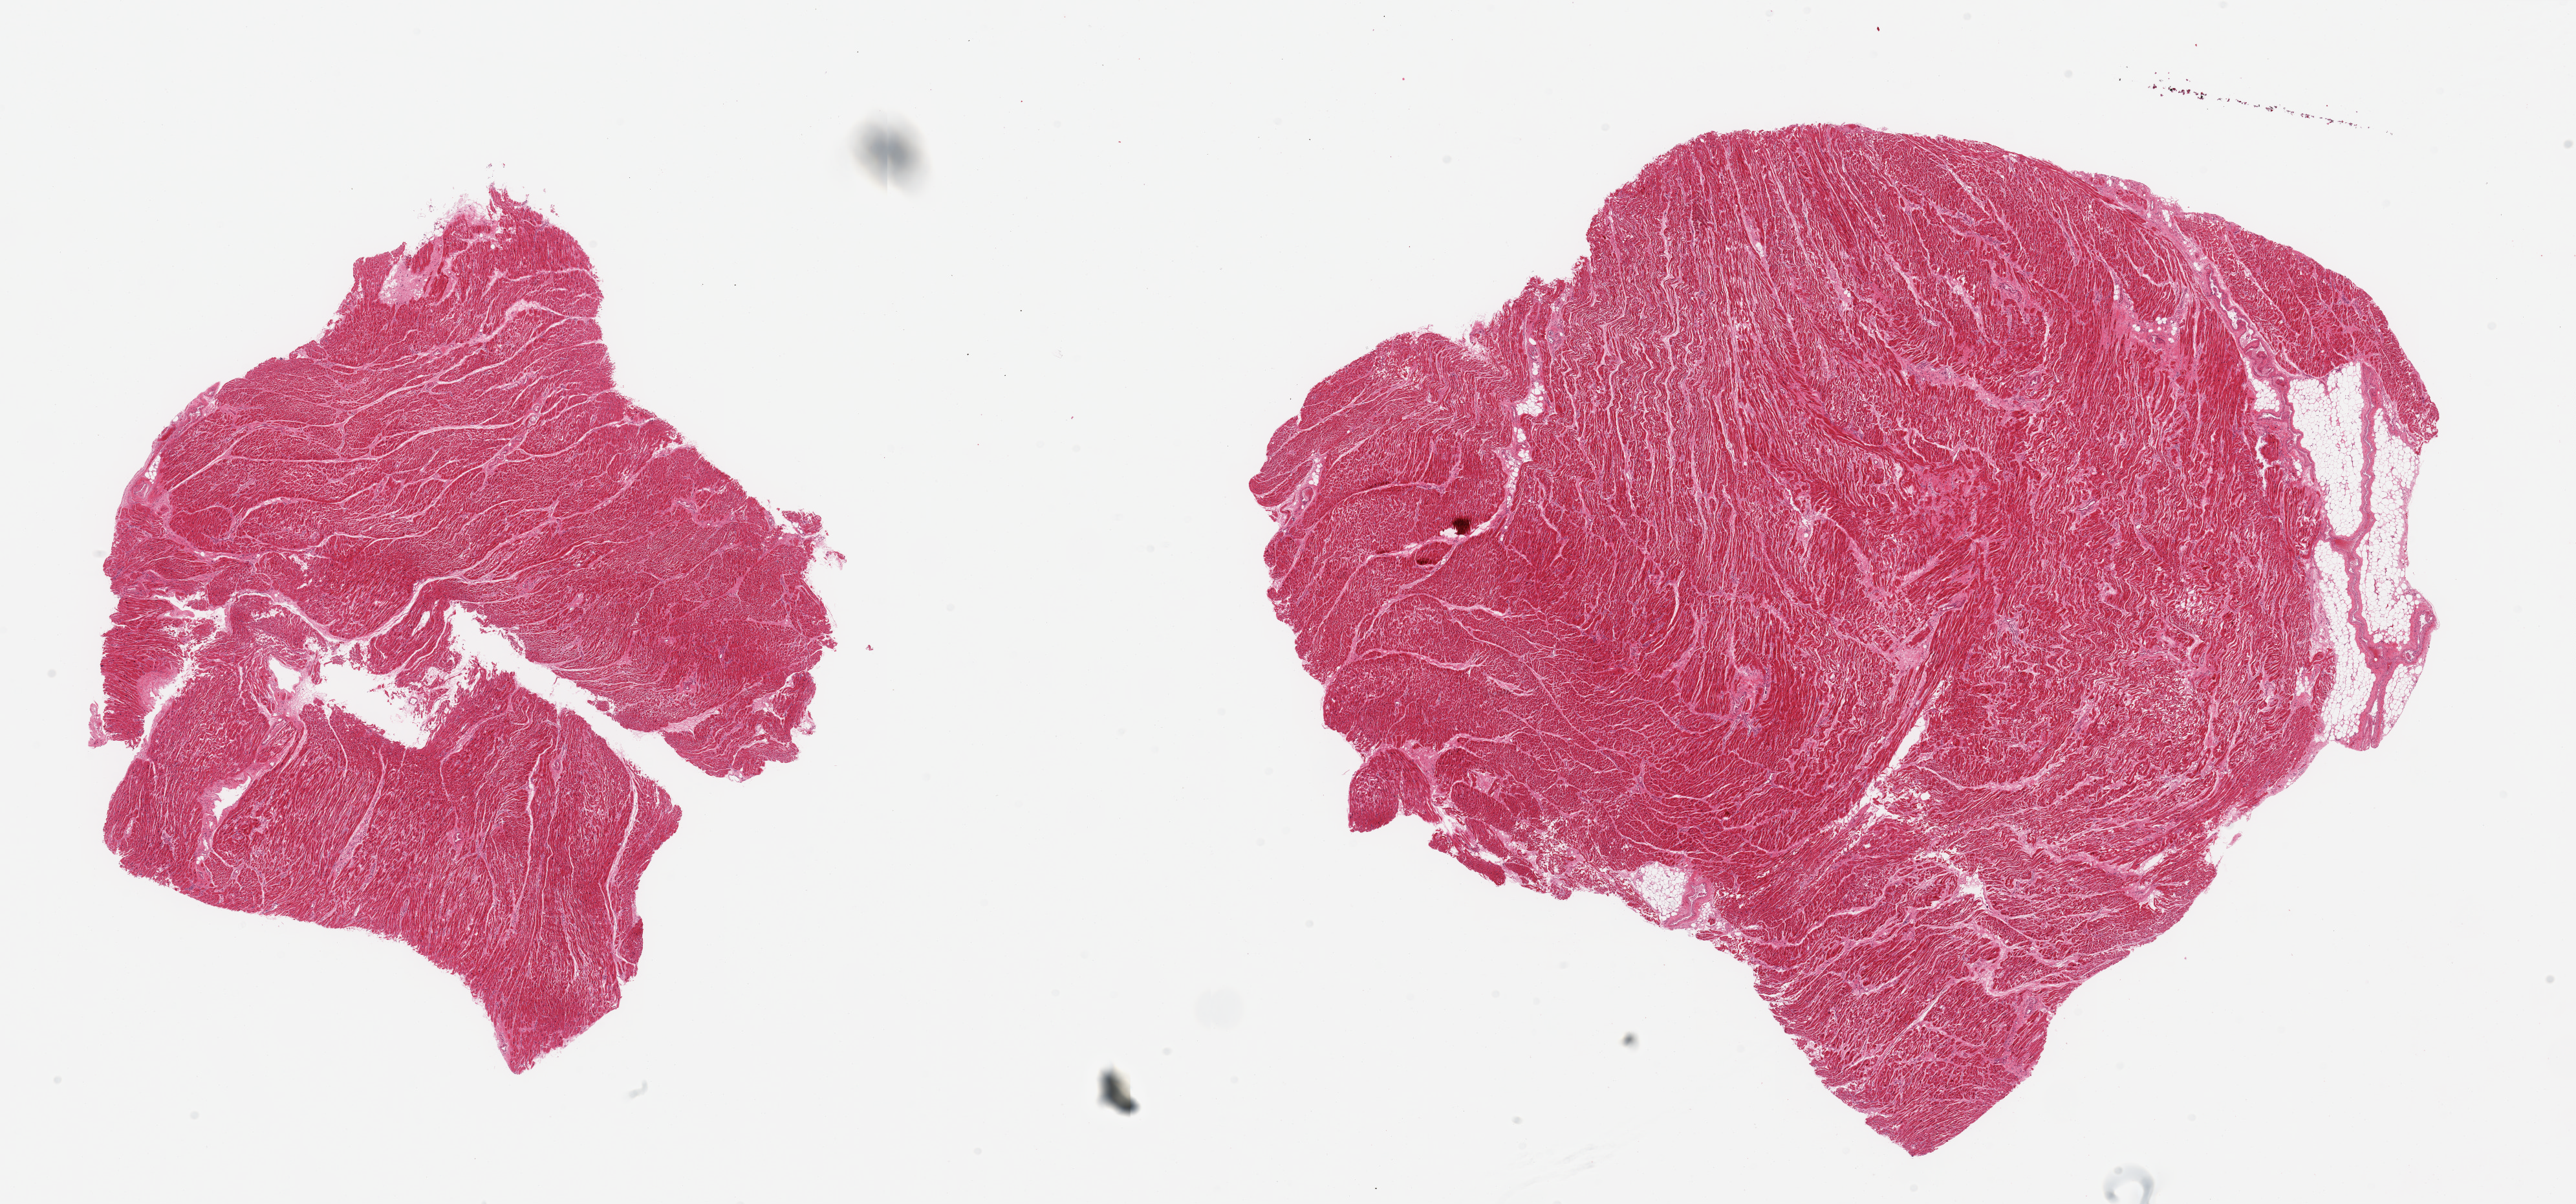
Whole-slide image, H&E stain, low-resolution overview of the scanned area, about 31.5 x 14.7 mm (slide scanned at 20x), PAXgene-fixed, paraffin-embedded tissue, target tissue: heart, tissue donor sample. Male donor.
Reviewer comment on this tissue sample: 2 pieces, moderate interstitial fibrosis/chronic ischemic changes.